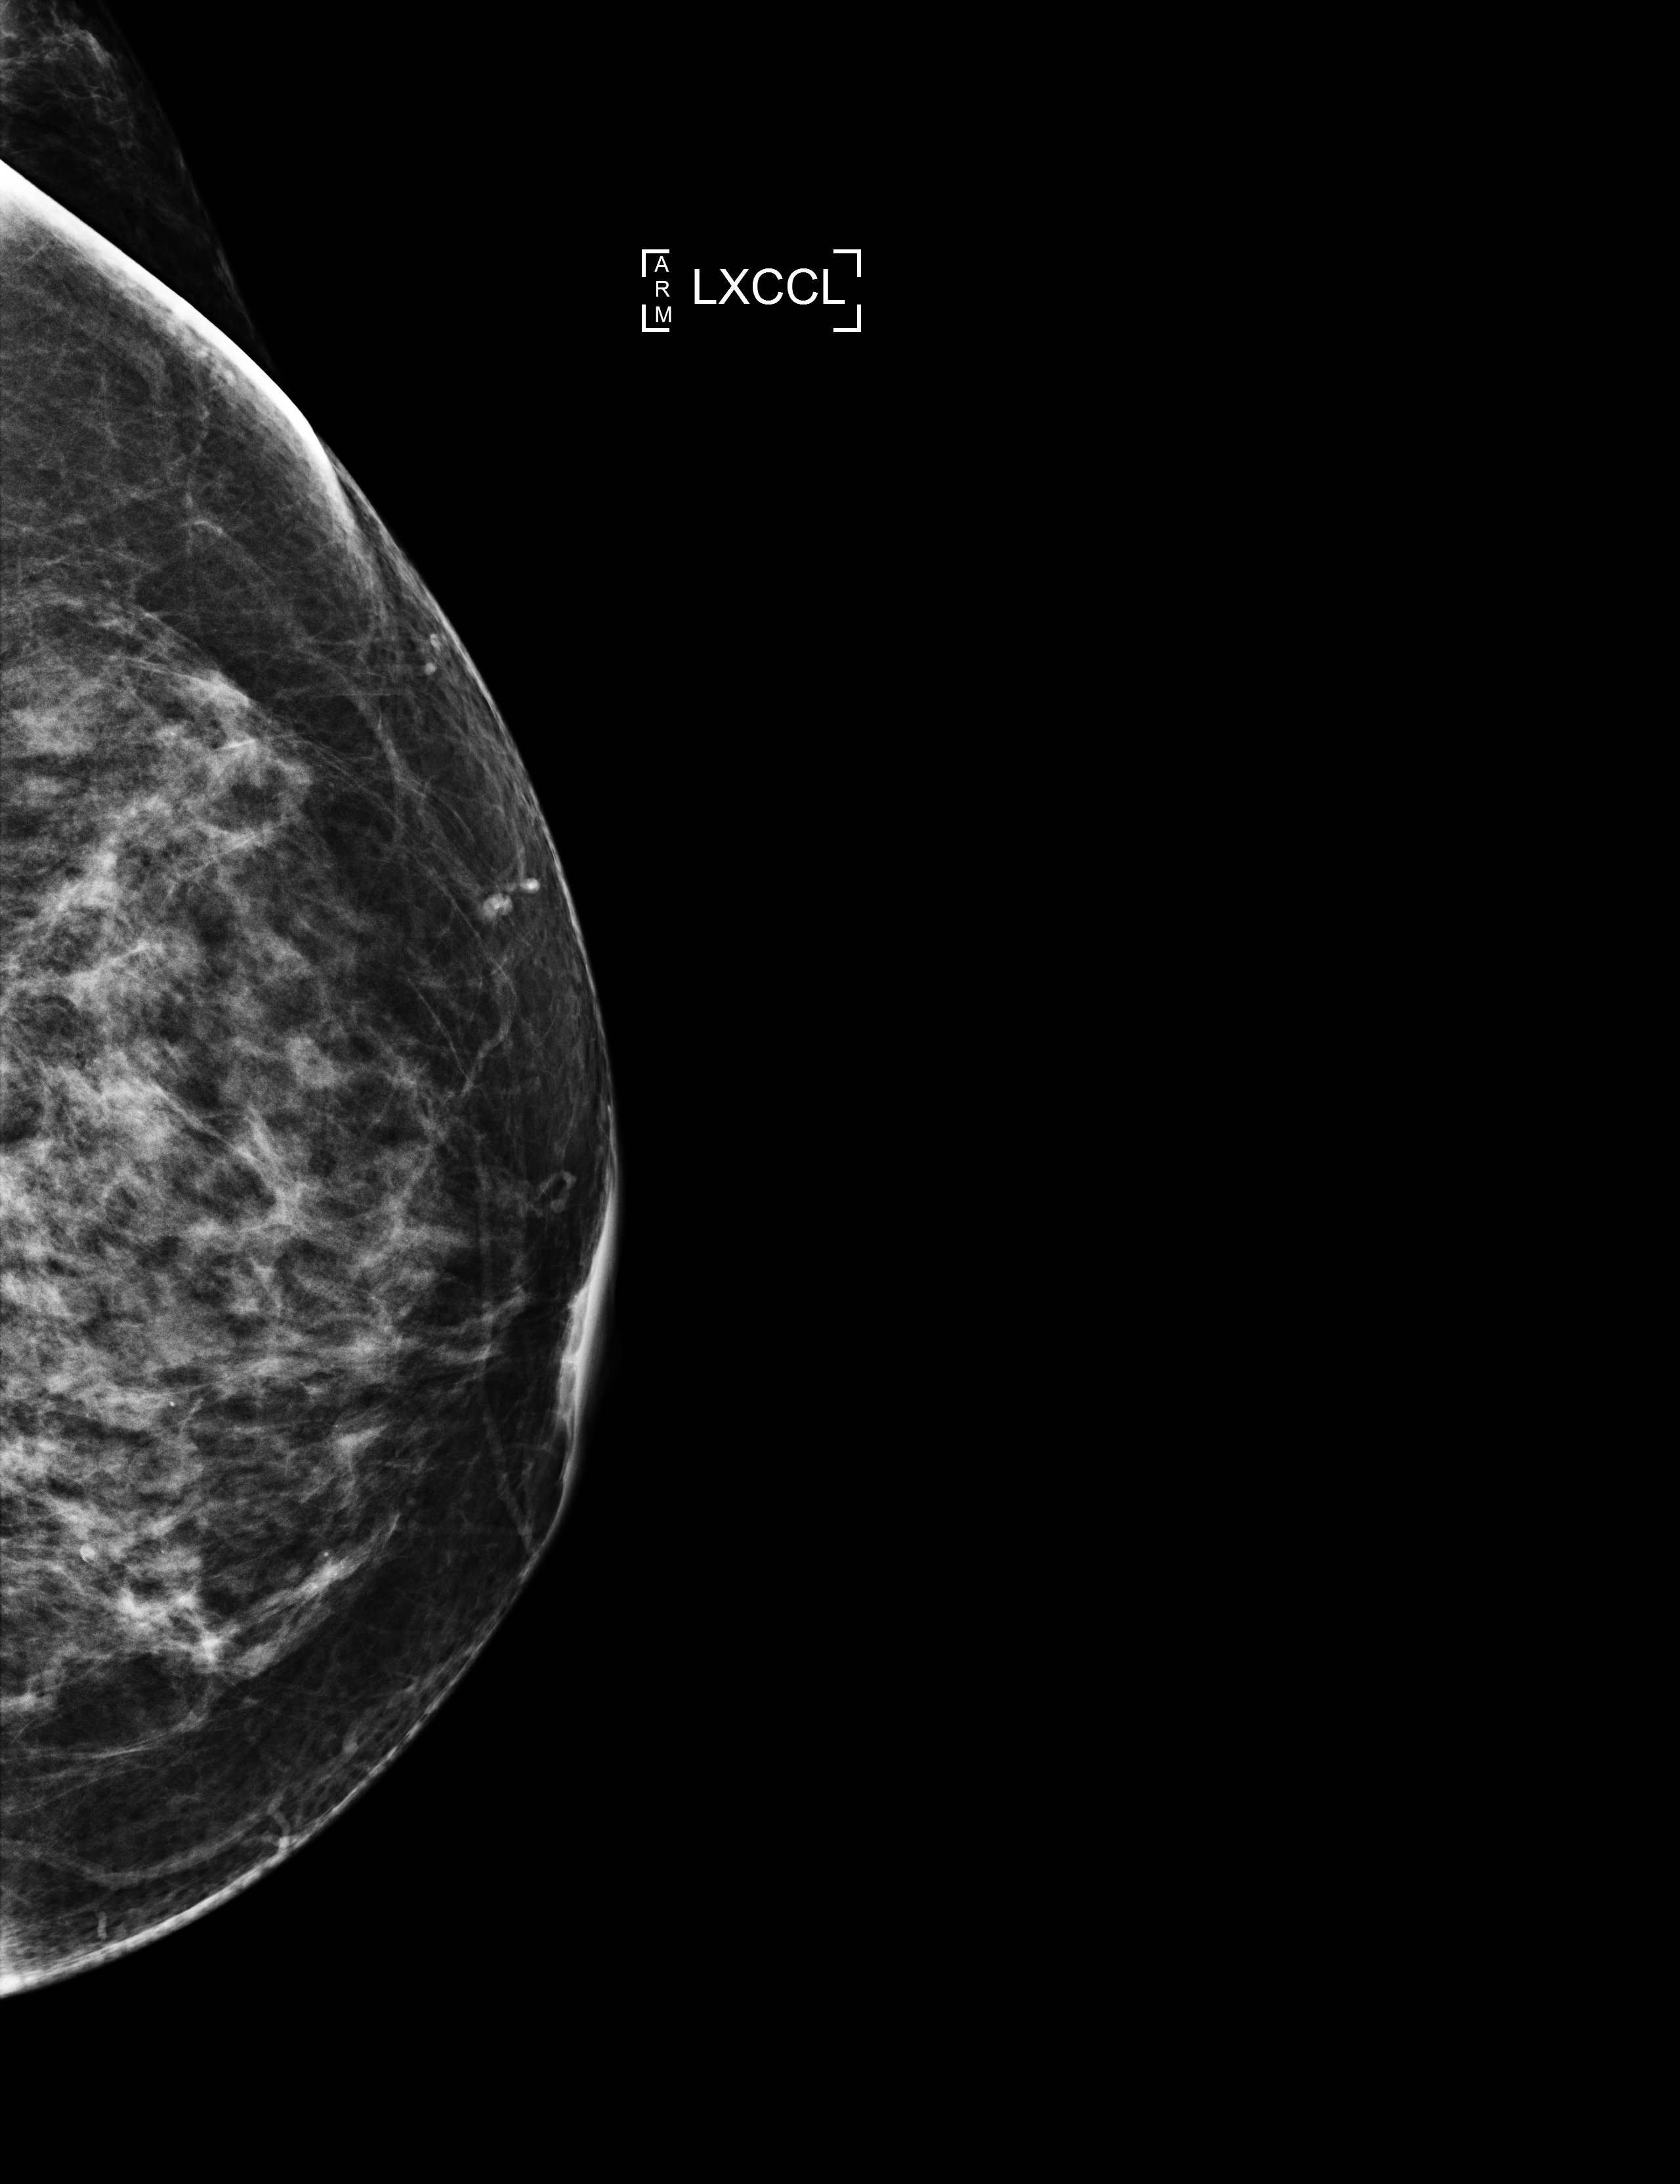
Annual screening mammography examination.
Image type: full-field digital mammogram. Breast: left. Projection: laterally exaggerated craniocaudal (XCCL) view.